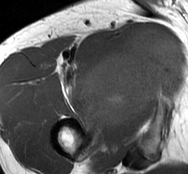
MRI of an extremity soft-tissue mass, one axial slice. Slice 59 of 93 in the series (ordered by position). MR volume resampled by the dataset authors to the PET/CT grid (not the native acquisition matrix). 3.27 mm slice thickness. 188 × 174 image matrix. Male patient. From the clinical record (not read from this slice): histological type: undifferentiated - pleiomorphic; grade: high; site of the primary tumour: right thigh.
Annotated regions visible in this slice (expert contour drawn on MRI and transferred to this co-registered scan by the dataset authors):
- gross tumour volume including surrounding oedema: bounding box [x1, y1, x2, y2] px = [79, 26, 183, 130]
- gross tumour volume (mass): [79, 26, 183, 130]